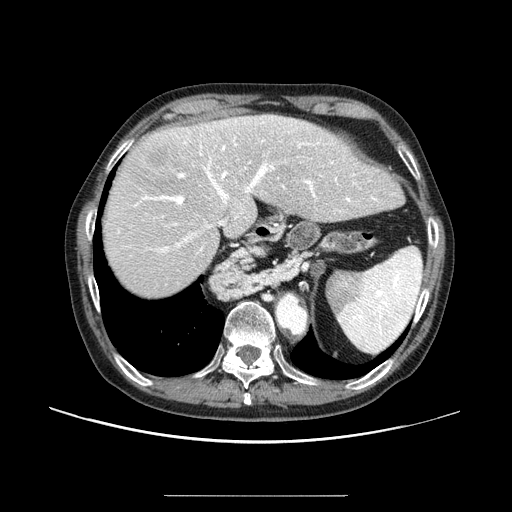
Contrast-enhanced abdominal CT (liver protocol), one axial slice. Position 68 of 91 along the scan axis. Reconstruction kernel STANDARD. One of 2 acquisitions stored at this slice position. Soft-tissue window (W 400 / L 40 HU). 512 × 512 image matrix, field of view 400 × 400 mm. From the clinical record (not read from this slice): diagnosis: hepatocellular carcinoma (patient treated with transarterial chemoembolisation; whether this scan precedes or follows treatment is not stated here); TNM stage (as recorded): Stage-I; Child-Pugh class: A; tumour differentiation: moderately differentiated; tumour nodularity: uninodular.
Structures marked on this image (semi-automatically segmented with operator editing):
- abdominal aorta: box from (x=277, y=296) to (x=305, y=332) px
- liver parenchyma outside the tumour (the mass and vessels are separate outlines, so this box may not span the whole liver): (x=102, y=114)–(x=402, y=296)
- mass: (x=139, y=131)–(x=183, y=174)
- liver vessels: (x=118, y=117)–(x=377, y=254)